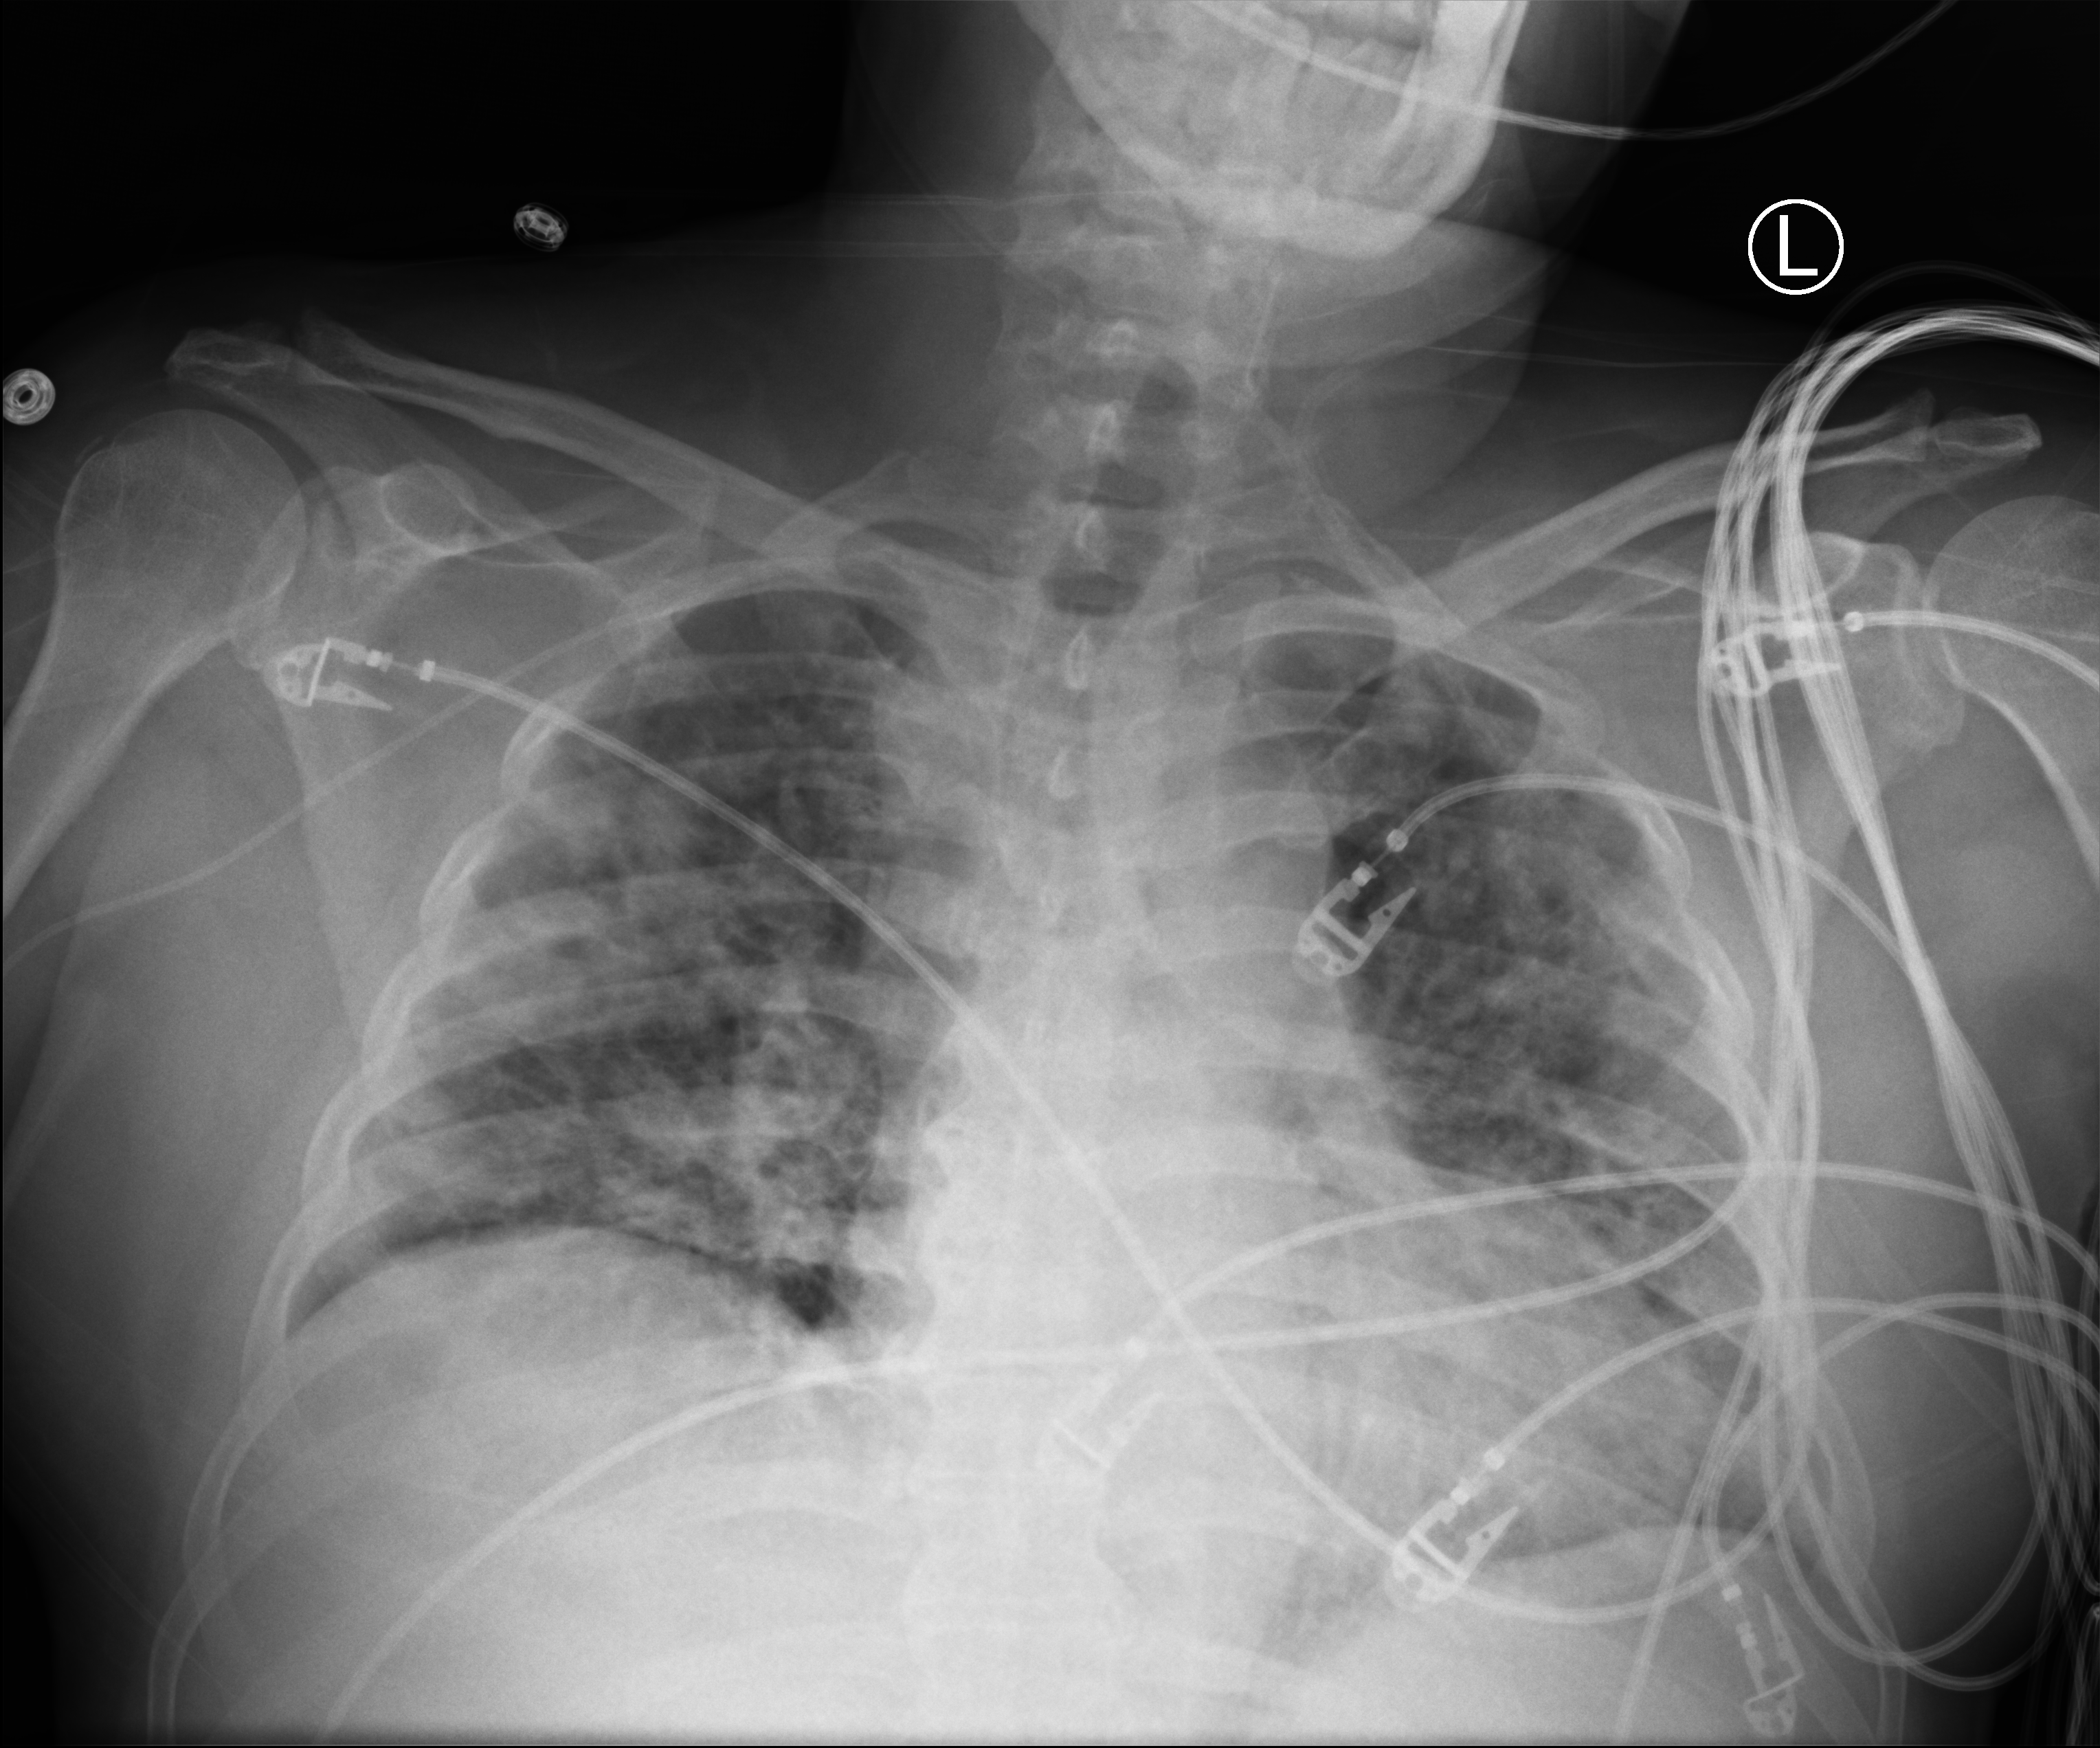
Chest X-ray (portable); anteroposterior (AP) projection. Patient hospitalised with COVID-19; male, aged 18–59 years.
Admission-level facts for this patient (not findings on this image; timing relative to this image not recorded):
- hypertension (admission record): yes
- admitted to intensive care during this hospital stay: yes
- mechanically ventilated during this hospital stay: yes